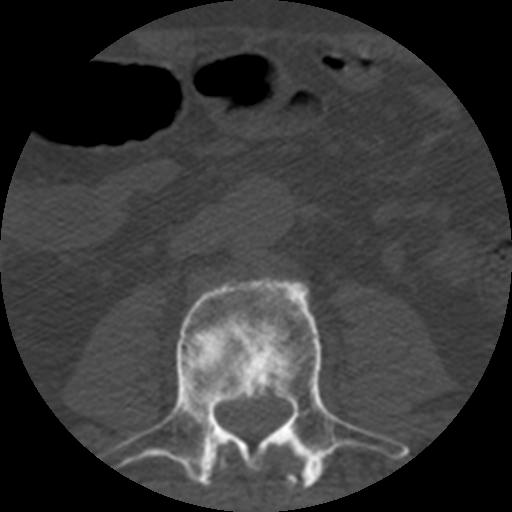
CT including the spine, one axial slice; slice 124 of 508 in the series (ordered by position); reconstruction kernel STANDARD; bone window (W 1800 / L 400 HU); 512 × 512 image matrix, field of view 160 × 160 mm. Patient age 57 years. Case-level facts recorded for this patient, not image findings: primary cancer: prostate.
Structures marked on this image (semi-automatic segmentation, software-assisted and operator-edited):
- L2 vertebra: bounding box [x1, y1, x2, y2] px = [213, 439, 308, 490]
- L3 vertebra: [97, 277, 409, 488]